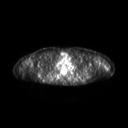
FDG PET of an extremity soft-tissue mass (from a PET/CT study), one axial slice; position 198 of 267 along the scan axis; 3.27 mm slice thickness; 128 × 128 image matrix, field of view 600 × 600 mm. Female patient, age 28 years. Case-level facts recorded for this patient, not image findings: histological type: malignant fibrous histiocytoma; grade: low; site of the primary tumour: left arm.
Structures marked on this image (expert contour drawn on MRI and transferred to this co-registered scan by the dataset authors):
- gross tumour volume (mass): bounding box [x1, y1, x2, y2] px = [104, 65, 106, 67]